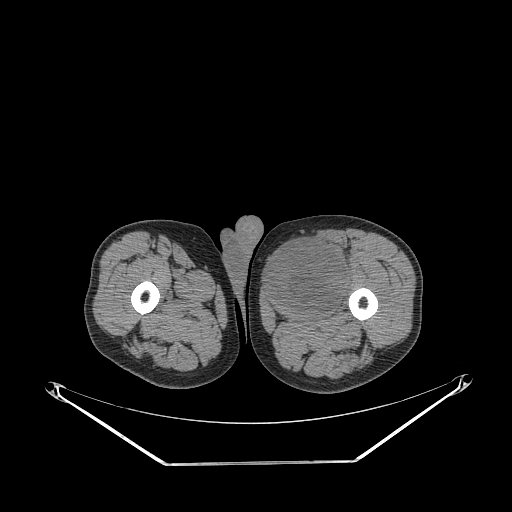
CT of an extremity soft-tissue mass (from a PET/CT study), one axial slice; position 254 of 267 along the scan axis; soft-tissue window (W 400 / L 40 HU); 512 × 512 image matrix, field of view 500 × 500 mm. Male patient. Case-level facts recorded for this patient, not image findings: histological type: pleiomorphic liposarcoma; grade: high; site of the primary tumour: left thigh.
Outlined on this slice (expert contour drawn on MRI and transferred to this co-registered scan by the dataset authors):
- gross tumour volume including surrounding oedema: box from (x=267, y=235) to (x=352, y=309) px
- gross tumour volume (mass): (x=267, y=240)–(x=348, y=309)